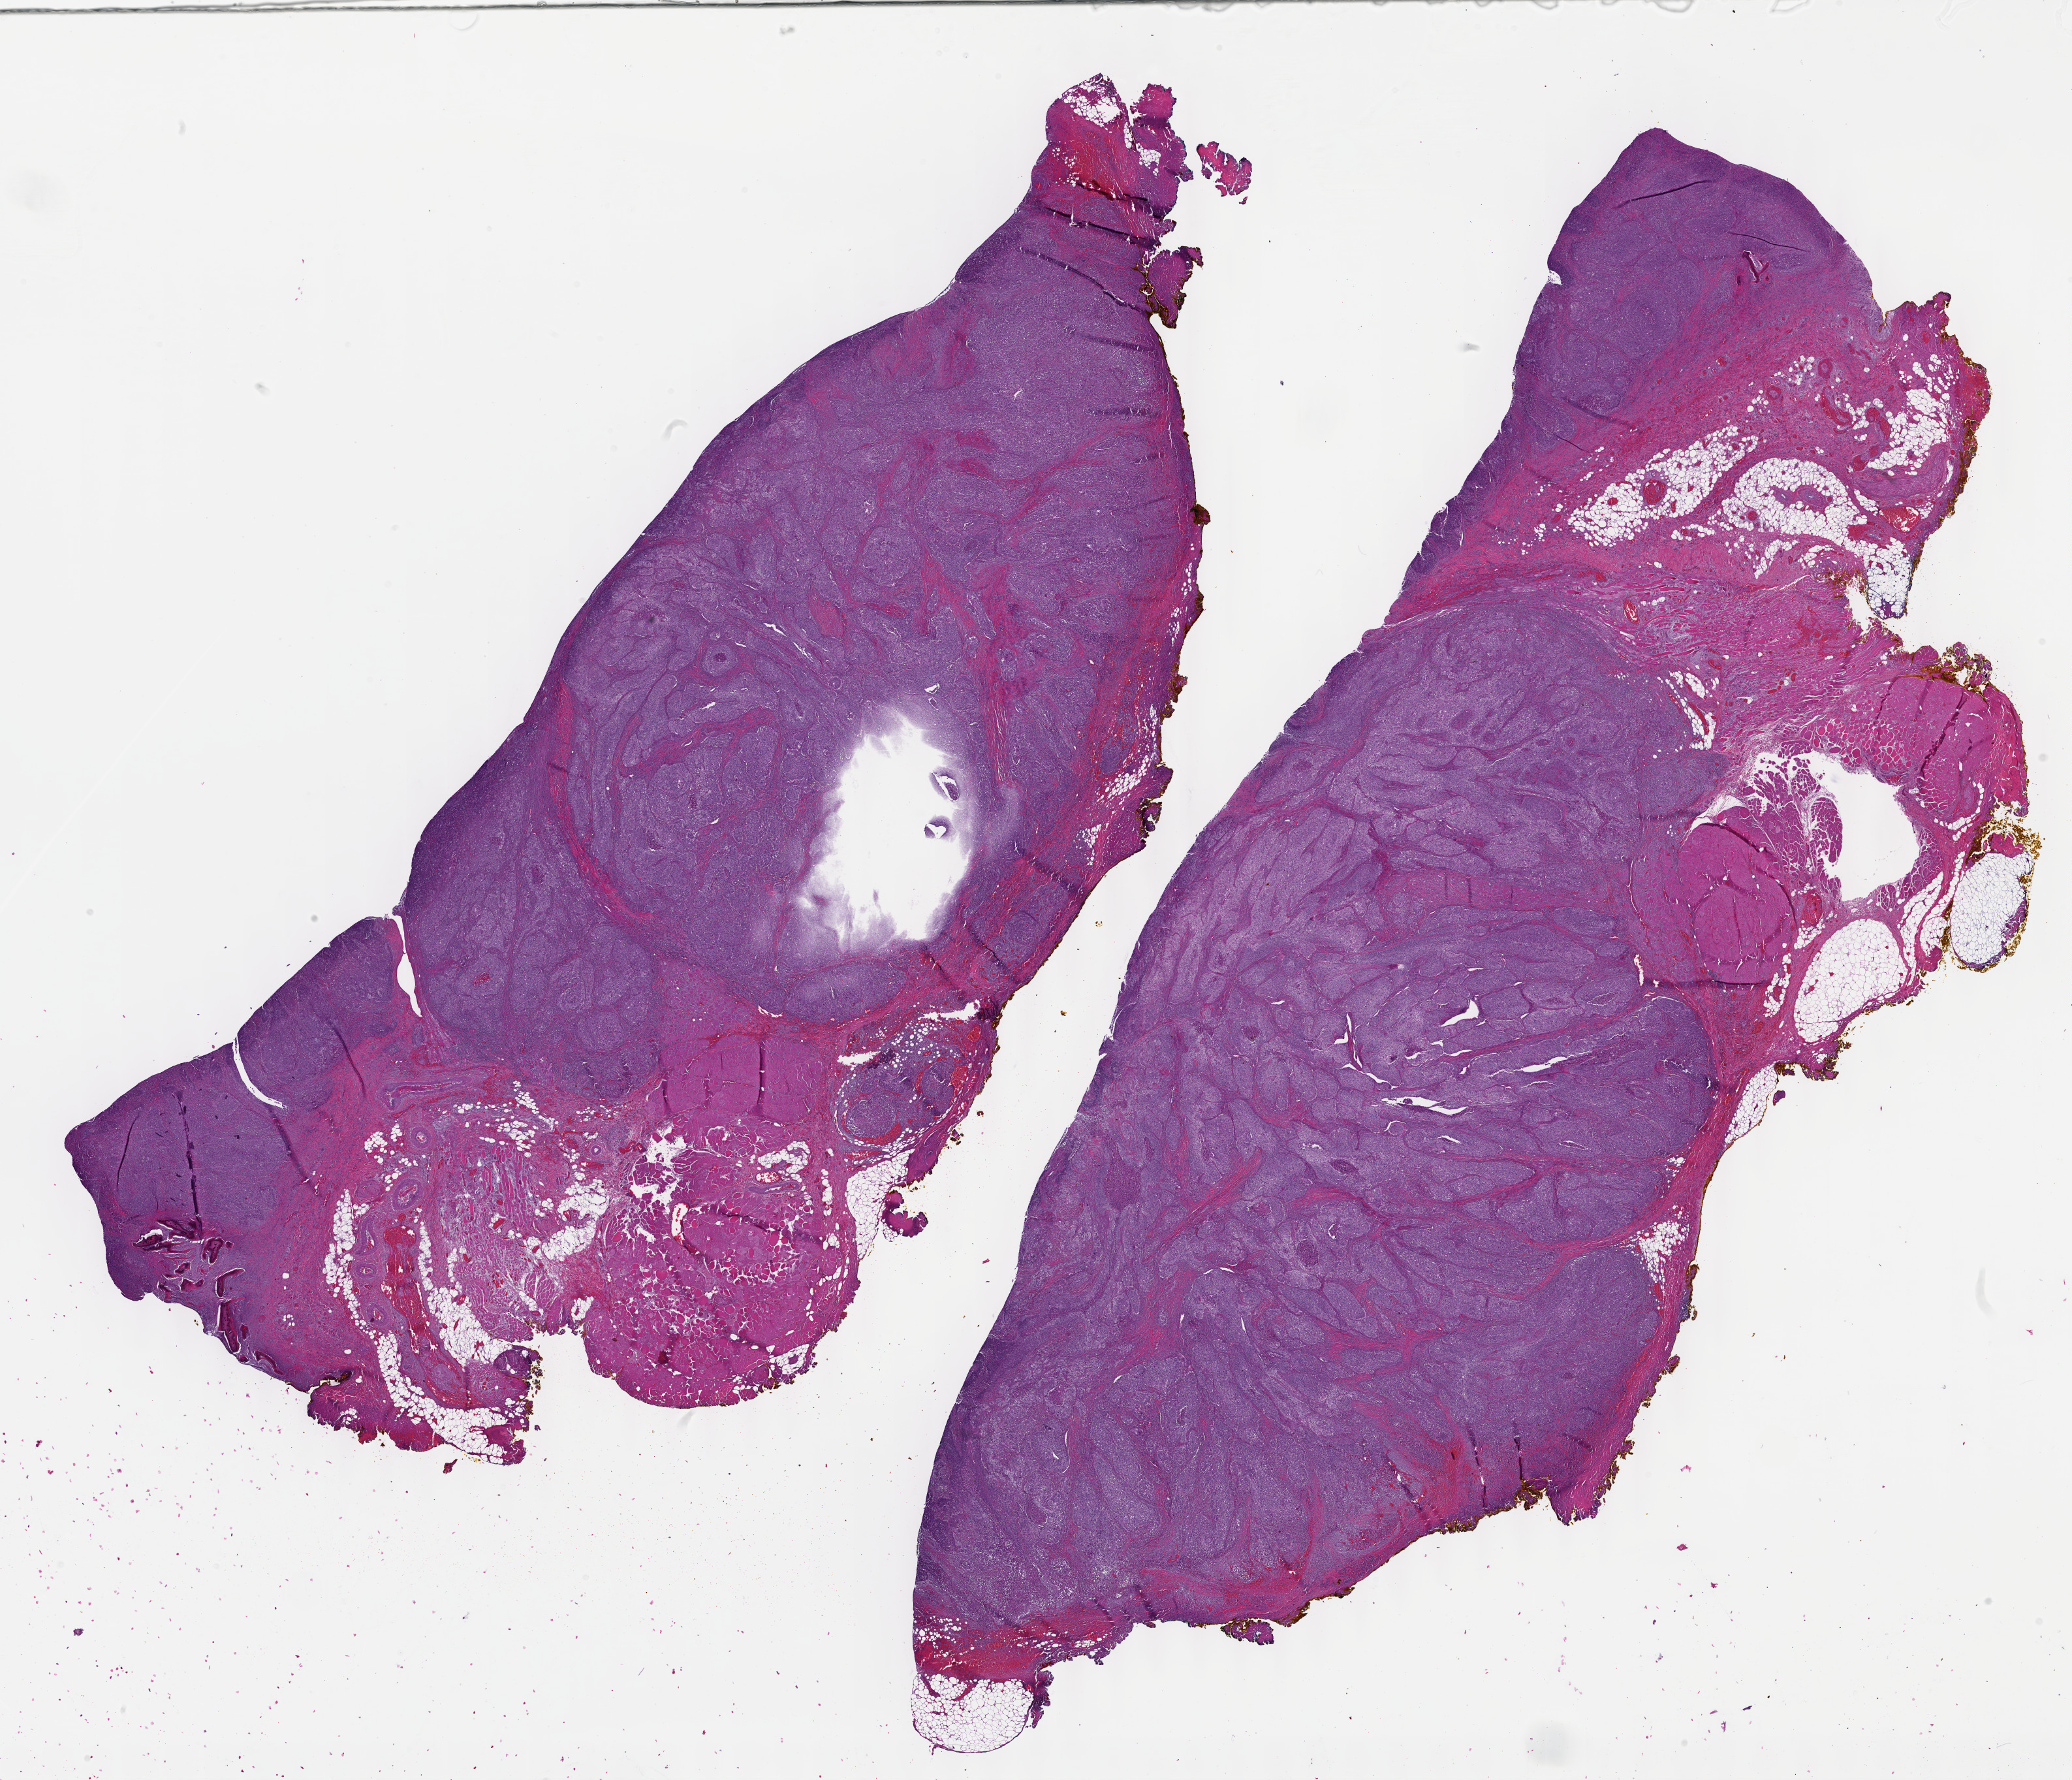
Whole-slide histology image, H&E, low-resolution overview of the scanned area, about 25.7 x 22.0 mm. FFPE section. Primary tumour sample from the head and neck. Patient: male, age at initial diagnosis 66 years. Histologic grade: G3 (poorly differentiated).
Diagnosis: Squamous cell carcinoma, NOS (overlapping lesion of lip, oral cavity and pharynx). AJCC pathologic stage: III.